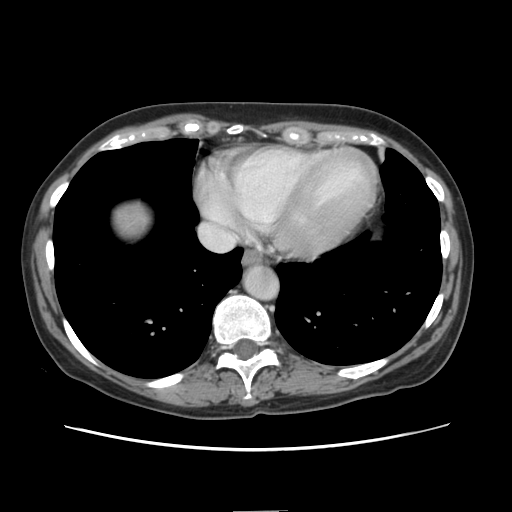
Contrast-enhanced abdominal CT, one axial slice. Position 134 of 141 along the scan axis. Intravenous contrast given. Soft-tissue window (W 400 / L 40 HU). 2.5 mm slice thickness. 512 × 512 image matrix. Female patient, age 63 years. From the clinical record (not read from this slice): diagnosis: colorectal cancer liver metastases, imaged before liver resection; multiple liver metastases: yes.
Structures marked on this image (manually delineated by an expert):
- liver: bounding box (x1, y1, x2, y2) in pixels: (111, 203, 150, 241)